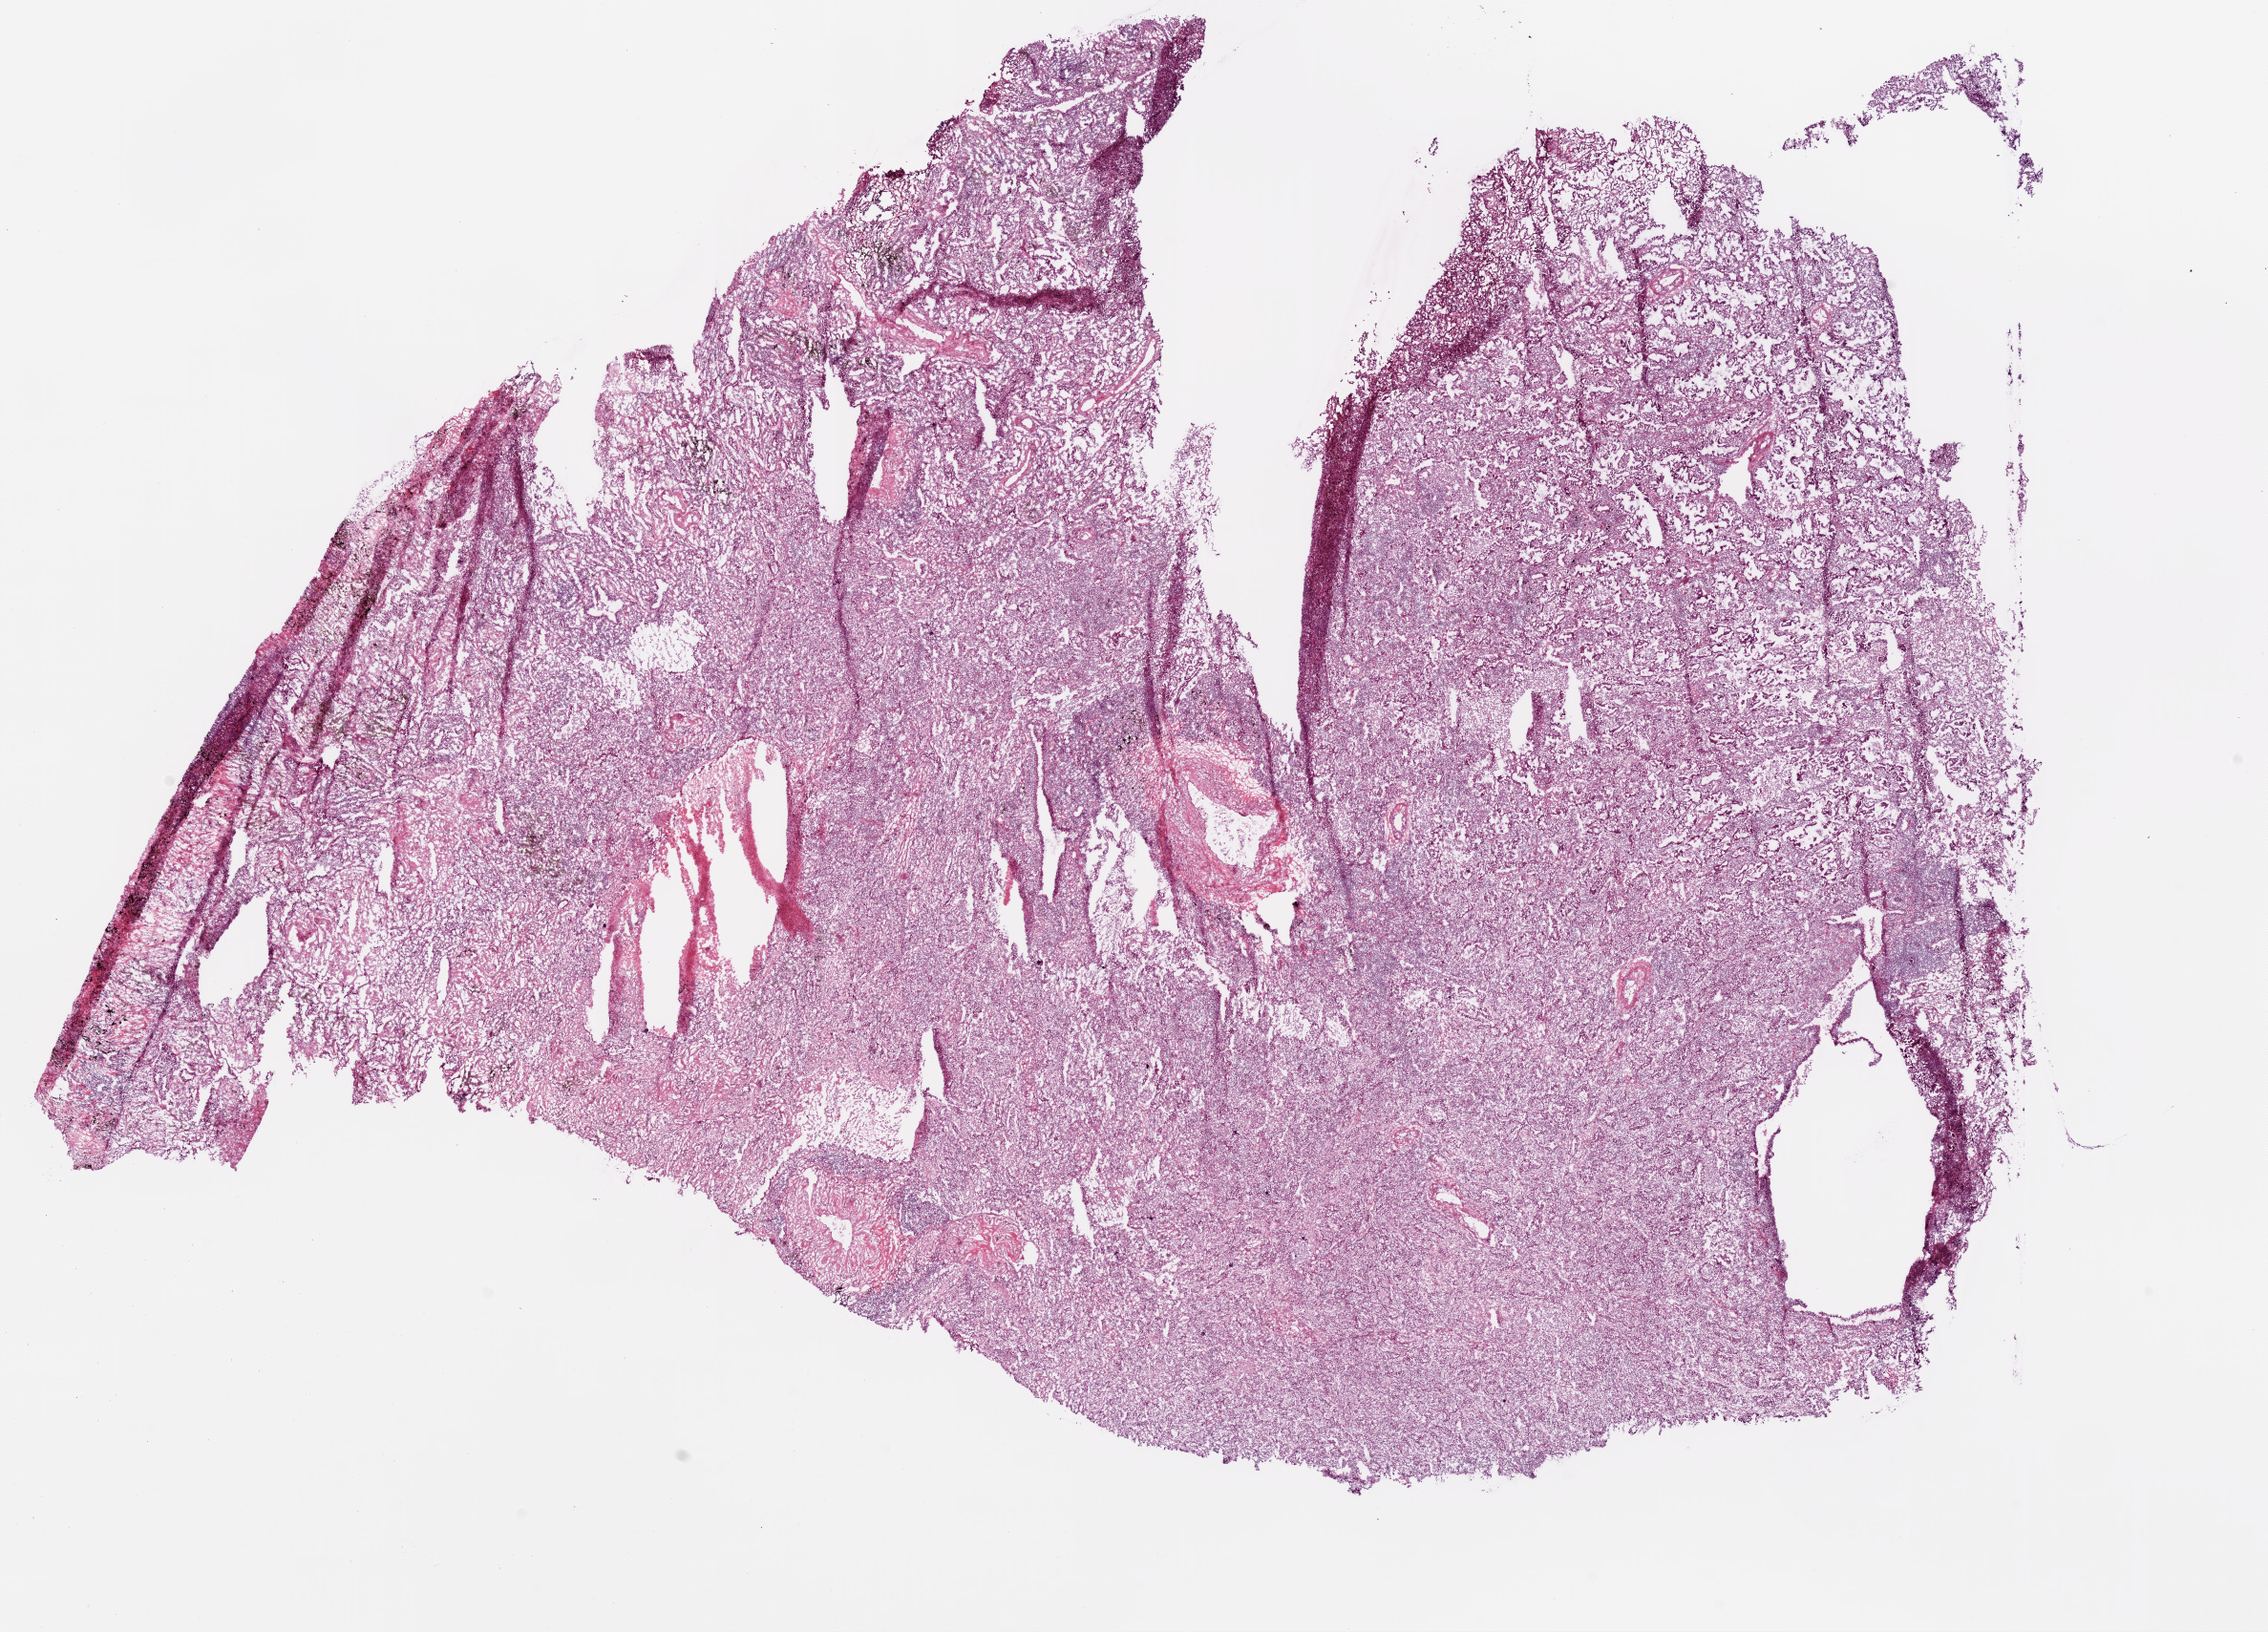
Digitized Hematoxylin and eosin (H&E) stained tissue section (whole slide), whole scanned area (about 19.1 x 13.7 mm) shown as a low-resolution overview, frozen section from the top of the tissue portion, lung, primary tumour sample. Female patient; age at initial diagnosis 59 years.
Pathologic diagnosis: Adenocarcinoma, NOS (lower lobe, lung).